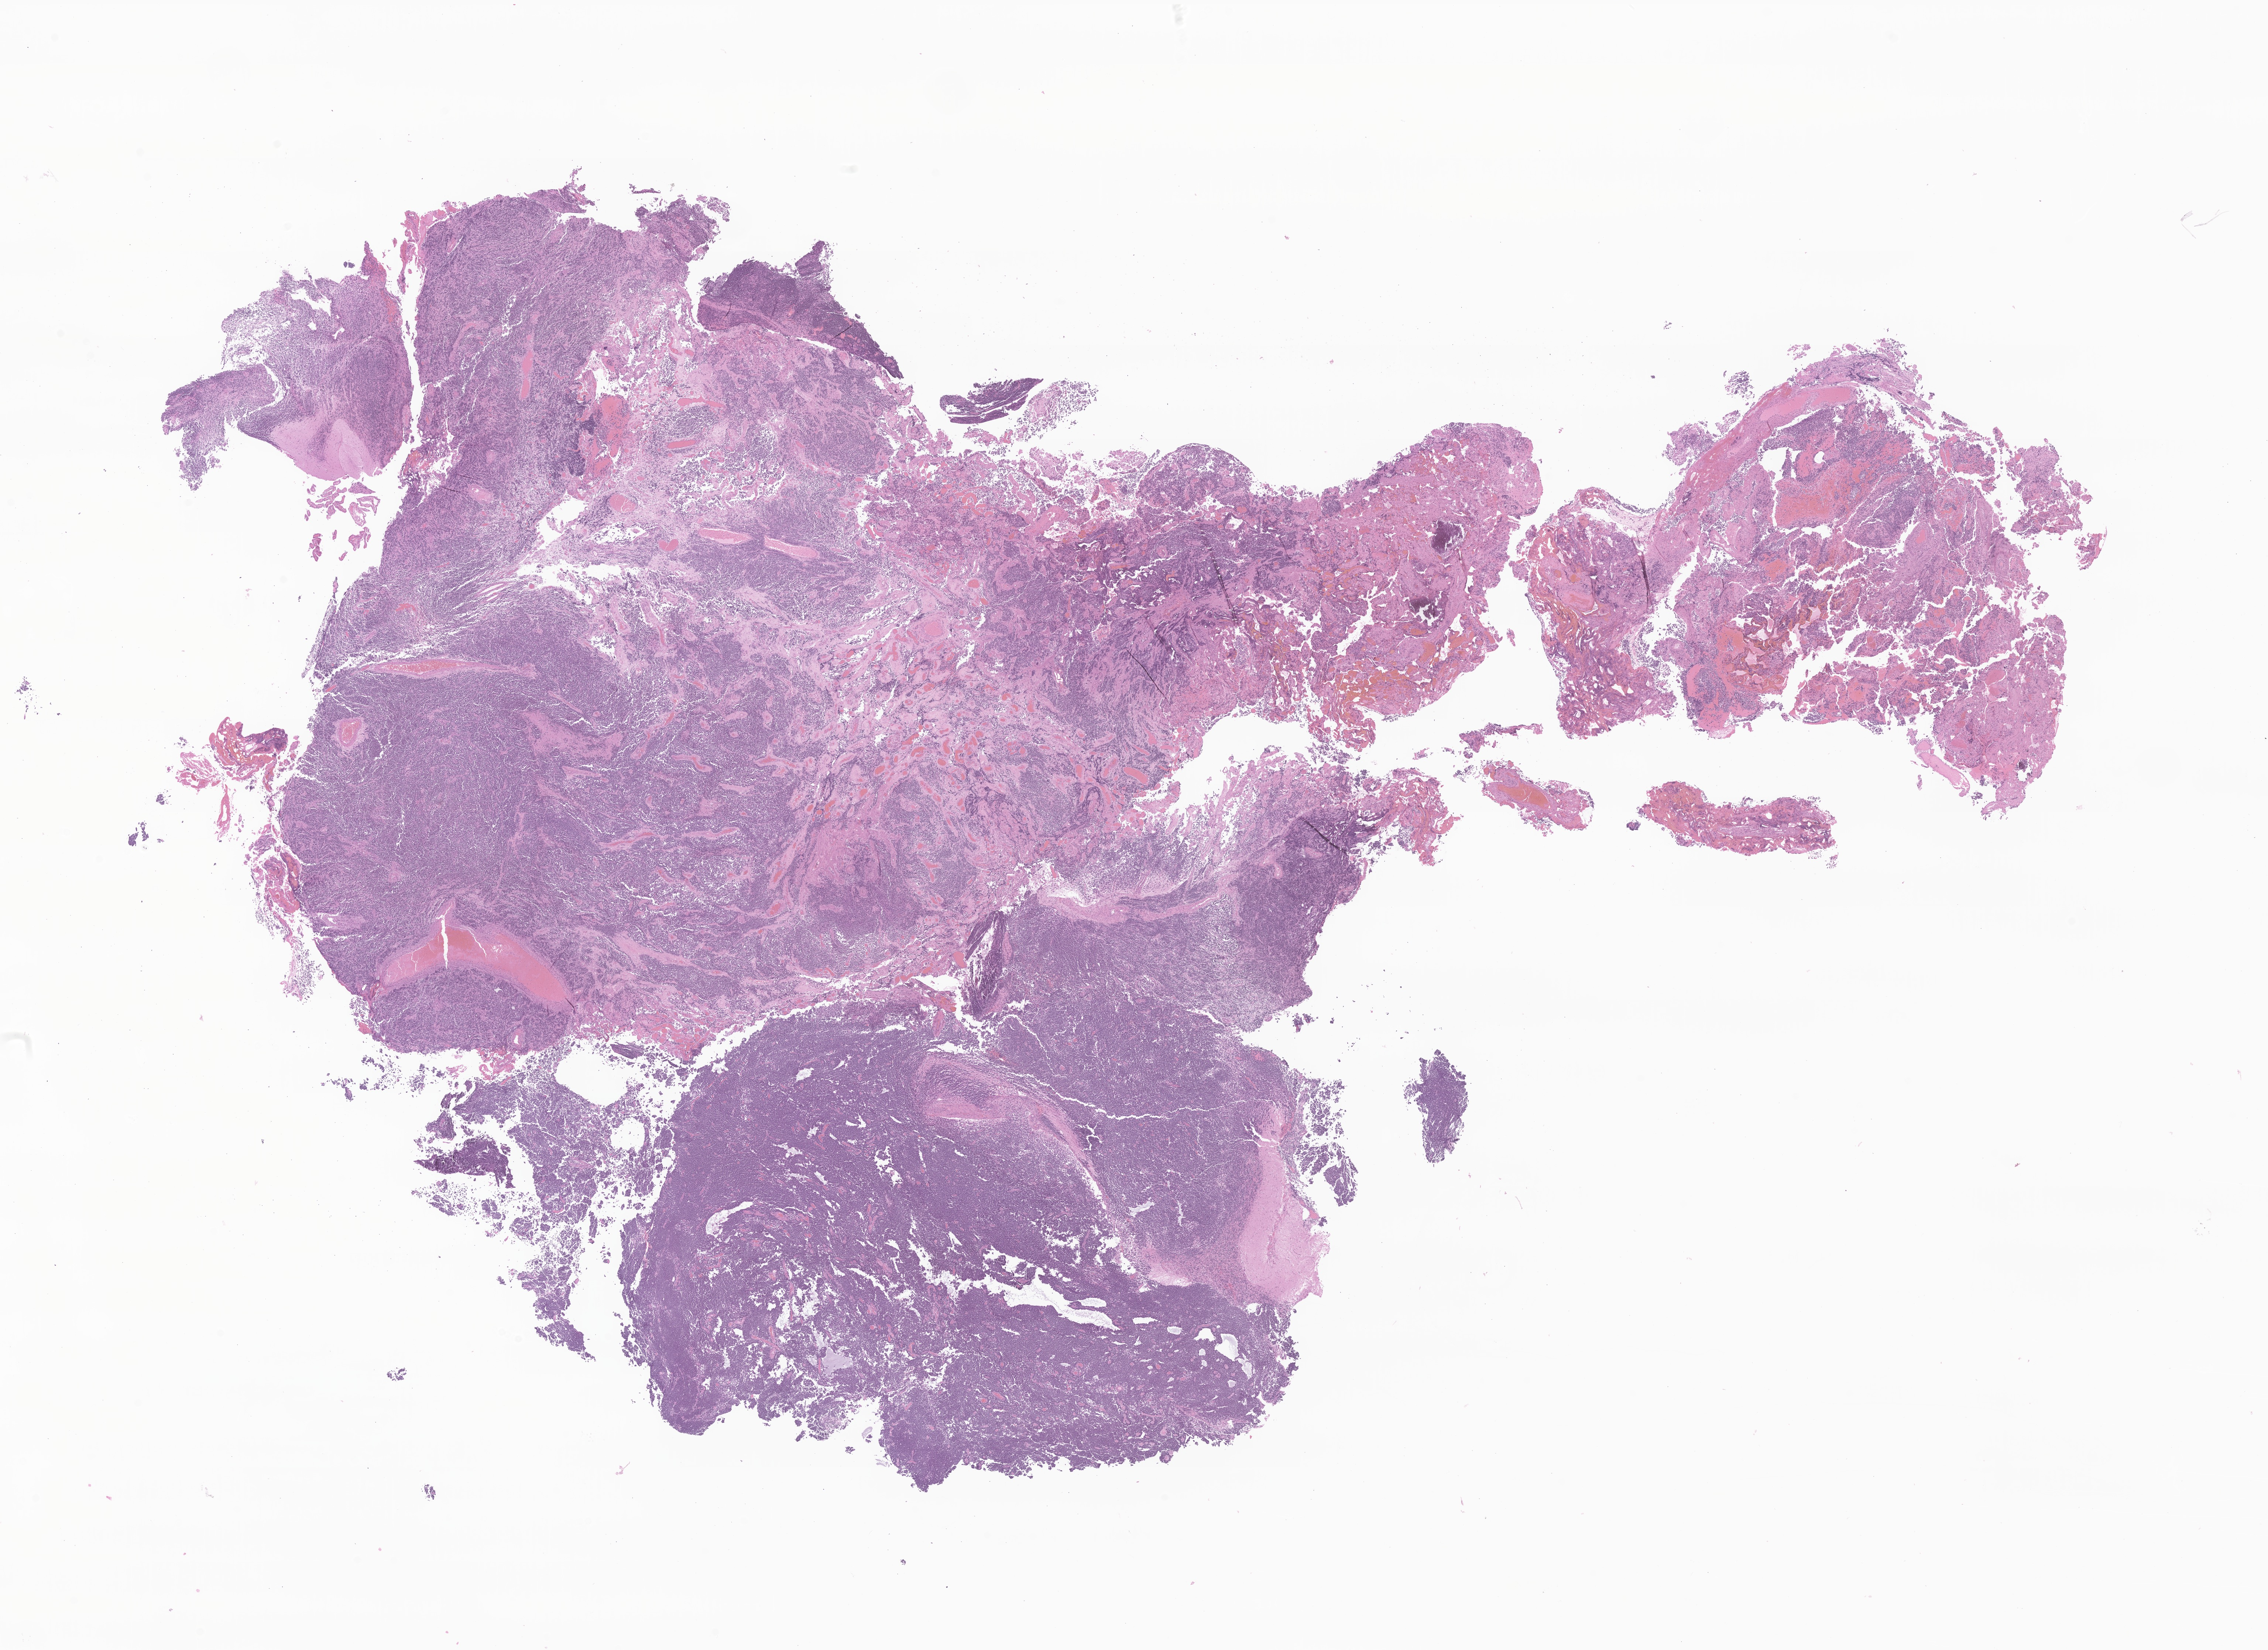
Digitized haematoxylin and eosin-stained section of tumor tissue from the cerebellum — shown as a low-resolution overview of the whole scanned area (about 25.9 x 18.8 mm), FFPE section. Female patient, age 50 months (4 years 2 months).
Diagnosis: Medulloblastoma, NOS.